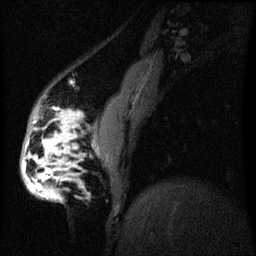
Breast MRI (dynamic contrast-enhanced), one sagittal slice; position 13 of 60 along the scan axis; dynamic contrast-enhanced series, image 2 of 3 at this slice position (ordered by acquisition); 1.5 T; TE 4.2 ms, TR 8 ms; 256 × 256 image matrix, field of view 200 × 200 mm. Patient: female, 50 years.
Outlined on this slice (semi-automatic segmentation, software-assisted and operator-edited):
- analysis volume of interest (the breast-tissue region the enhancement analysis was run in; not a lesion): bounding box <20,112,78,203> (left, top, right, bottom; pixels)
- tumour enhancement mask (voxels above the 70 % enhancement threshold inside the analysis volume of interest): <24,118,68,197>